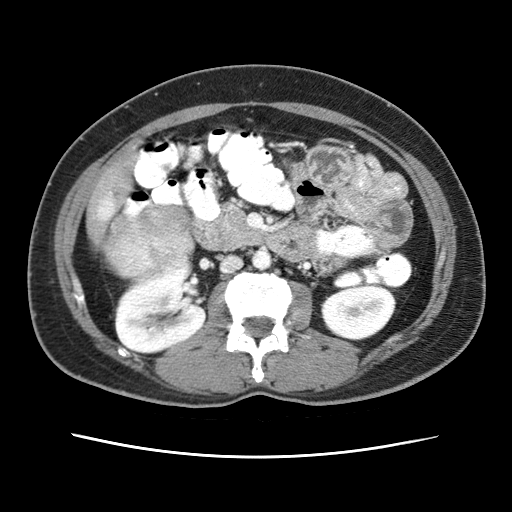
Contrast-enhanced abdominal CT (liver protocol), one axial slice. Slice 8 of 79 in the series (ordered by position). 120 kVp. Soft-tissue window (W 400 / L 40 HU). 2.5 mm slice thickness. 512 × 512 image matrix, field of view 340 × 340 mm. Case-level facts recorded for this patient, not image findings: diagnosis: hepatocellular carcinoma (patient treated with transarterial chemoembolisation; whether this scan precedes or follows treatment is not stated here); TNM stage (as recorded): Stage-I; Child-Pugh class: A; tumour nodularity: uninodular.
Annotated regions visible in this slice (semi-automatically segmented with operator editing):
- abdominal aorta: bounding box <253,251,271,271> (left, top, right, bottom; pixels)
- liver parenchyma outside the tumour (the mass and vessels are separate outlines, so this box may not span the whole liver): <100,158,132,192>
- mass: <103,203,193,278>